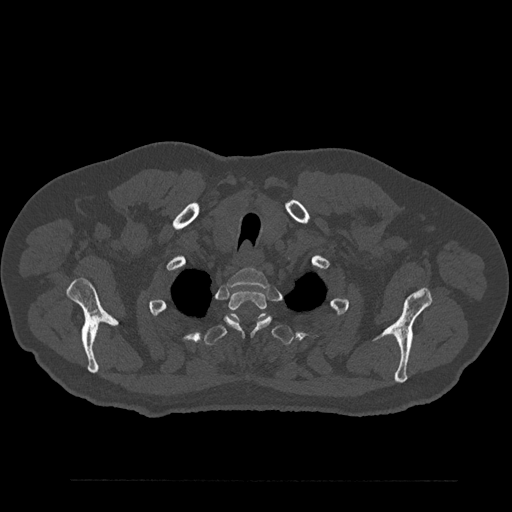
CT including the spine, one axial slice; position 712 of 797 along the scan axis; 120 kVp; bone window (W 1800 / L 400 HU); 0.5 mm slice thickness; 512 × 512 image matrix, field of view 430 × 430 mm. Male patient, age 61 years. Case-level facts recorded for this patient, not image findings: primary cancer: prostate.
Annotated regions visible in this slice (semi-automatically segmented with operator editing):
- T1 vertebra: bounding box [x1, y1, x2, y2] px = [227, 268, 269, 287]
- T2 vertebra: [224, 290, 272, 335]
- T3 vertebra: [205, 313, 294, 345]